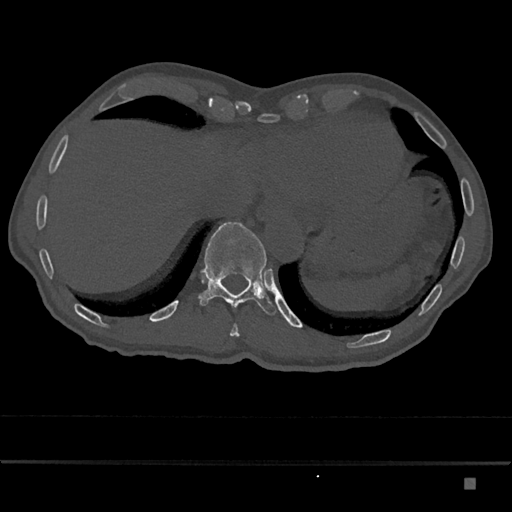
CT including the spine, one axial slice. Slice 686 of 797 in the series (ordered by position). Bone window (W 1800 / L 400 HU). 512 × 512 image matrix. Patient: male, 72 years. From the clinical record (not read from this slice): primary cancer: prostate.
Structures marked on this image (semi-automatically segmented with operator editing):
- T10 vertebra: bounding box [x1, y1, x2, y2] px = [230, 324, 239, 336]
- T11 vertebra: [199, 221, 276, 316]